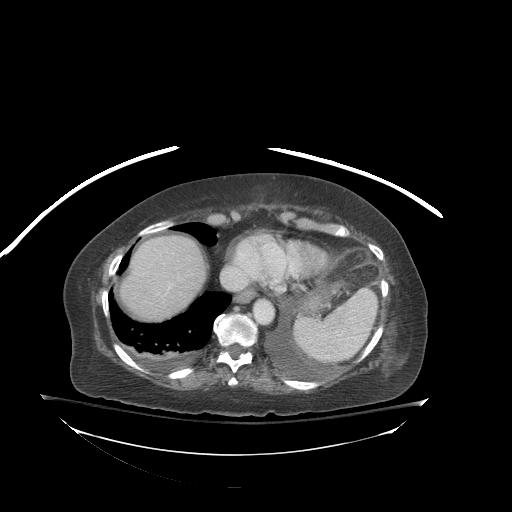
Contrast-enhanced abdominal CT (liver protocol), one axial slice. Reconstruction kernel STANDARD. 140 kVp. Soft-tissue window (W 400 / L 40 HU). 512 × 512 image matrix, field of view 500 × 500 mm. Case-level facts recorded for this patient, not image findings: diagnosis: hepatocellular carcinoma (patient treated with transarterial chemoembolisation; whether this scan precedes or follows treatment is not stated here); TNM stage (as recorded): Stage-I; Child-Pugh class: B; tumour nodularity: uninodular.
Outlined on this slice (semi-automatic segmentation, software-assisted and operator-edited):
- abdominal aorta: bounding box <255,301,273,323> (left, top, right, bottom; pixels)
- liver parenchyma outside the tumour (the mass and vessels are separate outlines, so this box may not span the whole liver): <120,234,206,320>